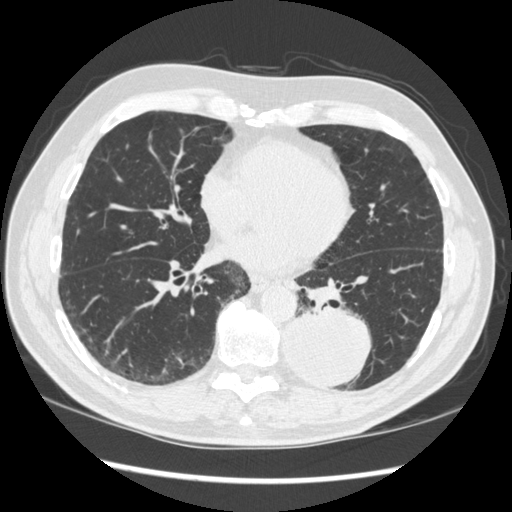
Low-dose screening chest CT, axial slice; baseline annual screen; lung window (W 1500 / L -600 HU); 1.25 mm slice thickness; 120 kVp; slice 135 of 348 in the series. Male participant, aged 72 years at enrolment.
Expert-annotated lung lesion, bounding box <270,299,374,389> (left, top, right, bottom; pixels). The screening reader recorded 2 non-calcified nodules or masses ≥4 mm on this exam (left lower lobe, right middle lobe); which of them this box marks is not recorded. Later outcome: lung cancer diagnosed 37 days after this screen — squamous cell carcinoma, NOS, left lower lobe, stage IIIA (AJCC 6th edition), 60 mm at pathology.